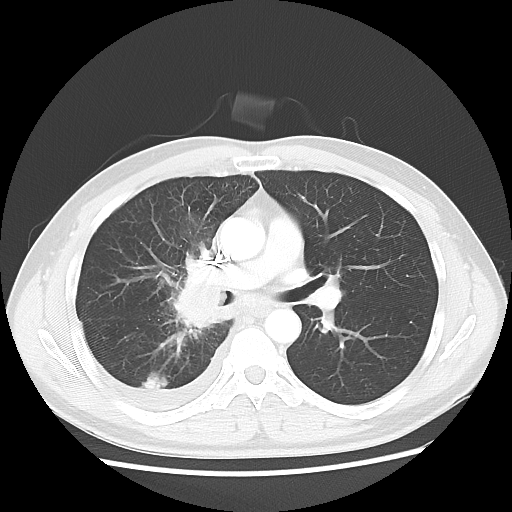
Chest CT, one axial slice. Reconstruction kernel LUNG. 120 kVp. Lung window (W 1500 / L -600 HU). 5 mm slice thickness. 512 × 512 image matrix. Male patient, age 46 years. From the clinical record (not read from this slice): clinical TNM (as recorded): T2 N3 M1.
Outlined on this slice (rectangle marked by the reading radiologist):
- lung tumour (recorded histology: adenocarcinoma): bounding box [x1, y1, x2, y2] px = [156, 248, 229, 344]